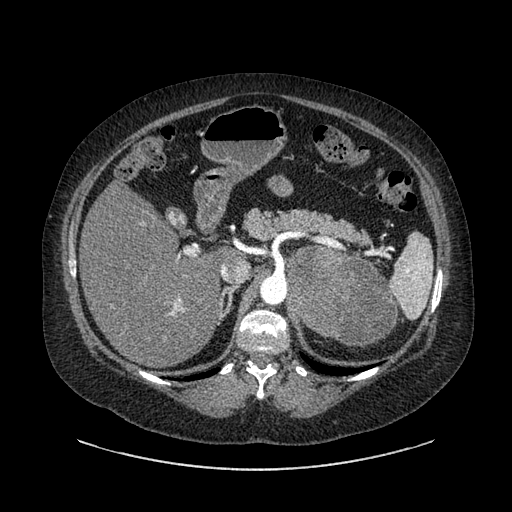
Contrast-enhanced abdominal CT, one axial slice; slice 585 of 769 in the series (ordered by position); reconstruction kernel SOFT; 120 kVp; intravenous contrast given; soft-tissue window (W 400 / L 40 HU); 512 × 512 image matrix, field of view 460 × 460 mm. Female patient, age 61 years. Case-level facts recorded for this patient, not image findings: diagnosis: adrenocortical carcinoma; tumour side: left adrenal; tumour size at pathology: 13 cm; Ki-67 index: 79 %; stage (as recorded): 2.
Annotated regions visible in this slice (semi-automatically segmented with operator editing):
- mass: bounding box [x1, y1, x2, y2] px = [287, 249, 396, 345]